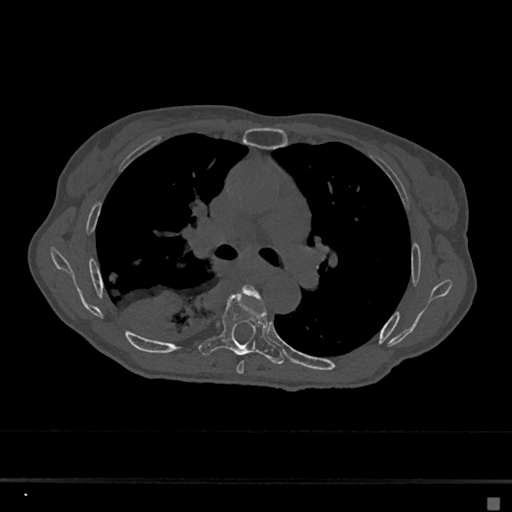
CT including the spine, one axial slice. Slice 429 of 797 in the series (ordered by position). Reconstruction kernel Br40s/3. 120 kVp. Bone window (W 1800 / L 400 HU). 0.5 mm slice thickness. 512 × 512 image matrix, field of view 360 × 360 mm. Patient: female, 68 years. Case-level facts recorded for this patient, not image findings: primary cancer: renal.
Structures marked on this image (semi-automatic segmentation, software-assisted and operator-edited):
- T5 vertebra: bounding box <236,285,262,375> (left, top, right, bottom; pixels)
- T6 vertebra: <199,290,284,364>